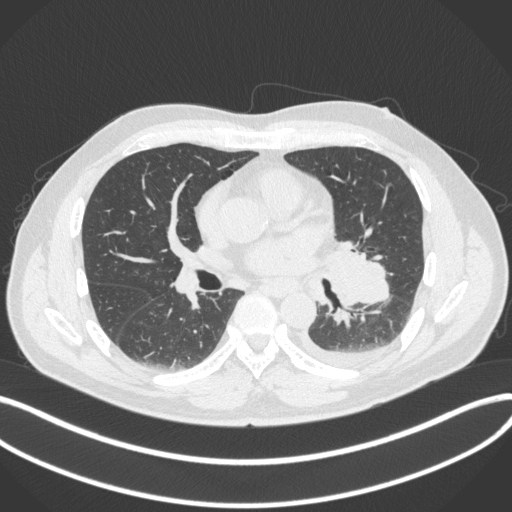
Chest CT, one axial slice. Slice 187 of 350 in the series (ordered by position). Reconstruction kernel B31f. 120 kVp. Lung window (W 1500 / L -600 HU). 512 × 512 image matrix, field of view 400 × 400 mm. Male patient, age 58 years. From the clinical record (not read from this slice): clinical TNM (as recorded): T3 N1 M1b; histopathological grade: G3.
Structures marked on this image (bounding box drawn by a radiologist):
- lung tumour (recorded histology: small cell carcinoma): bounding box <319,241,394,312> (left, top, right, bottom; pixels)